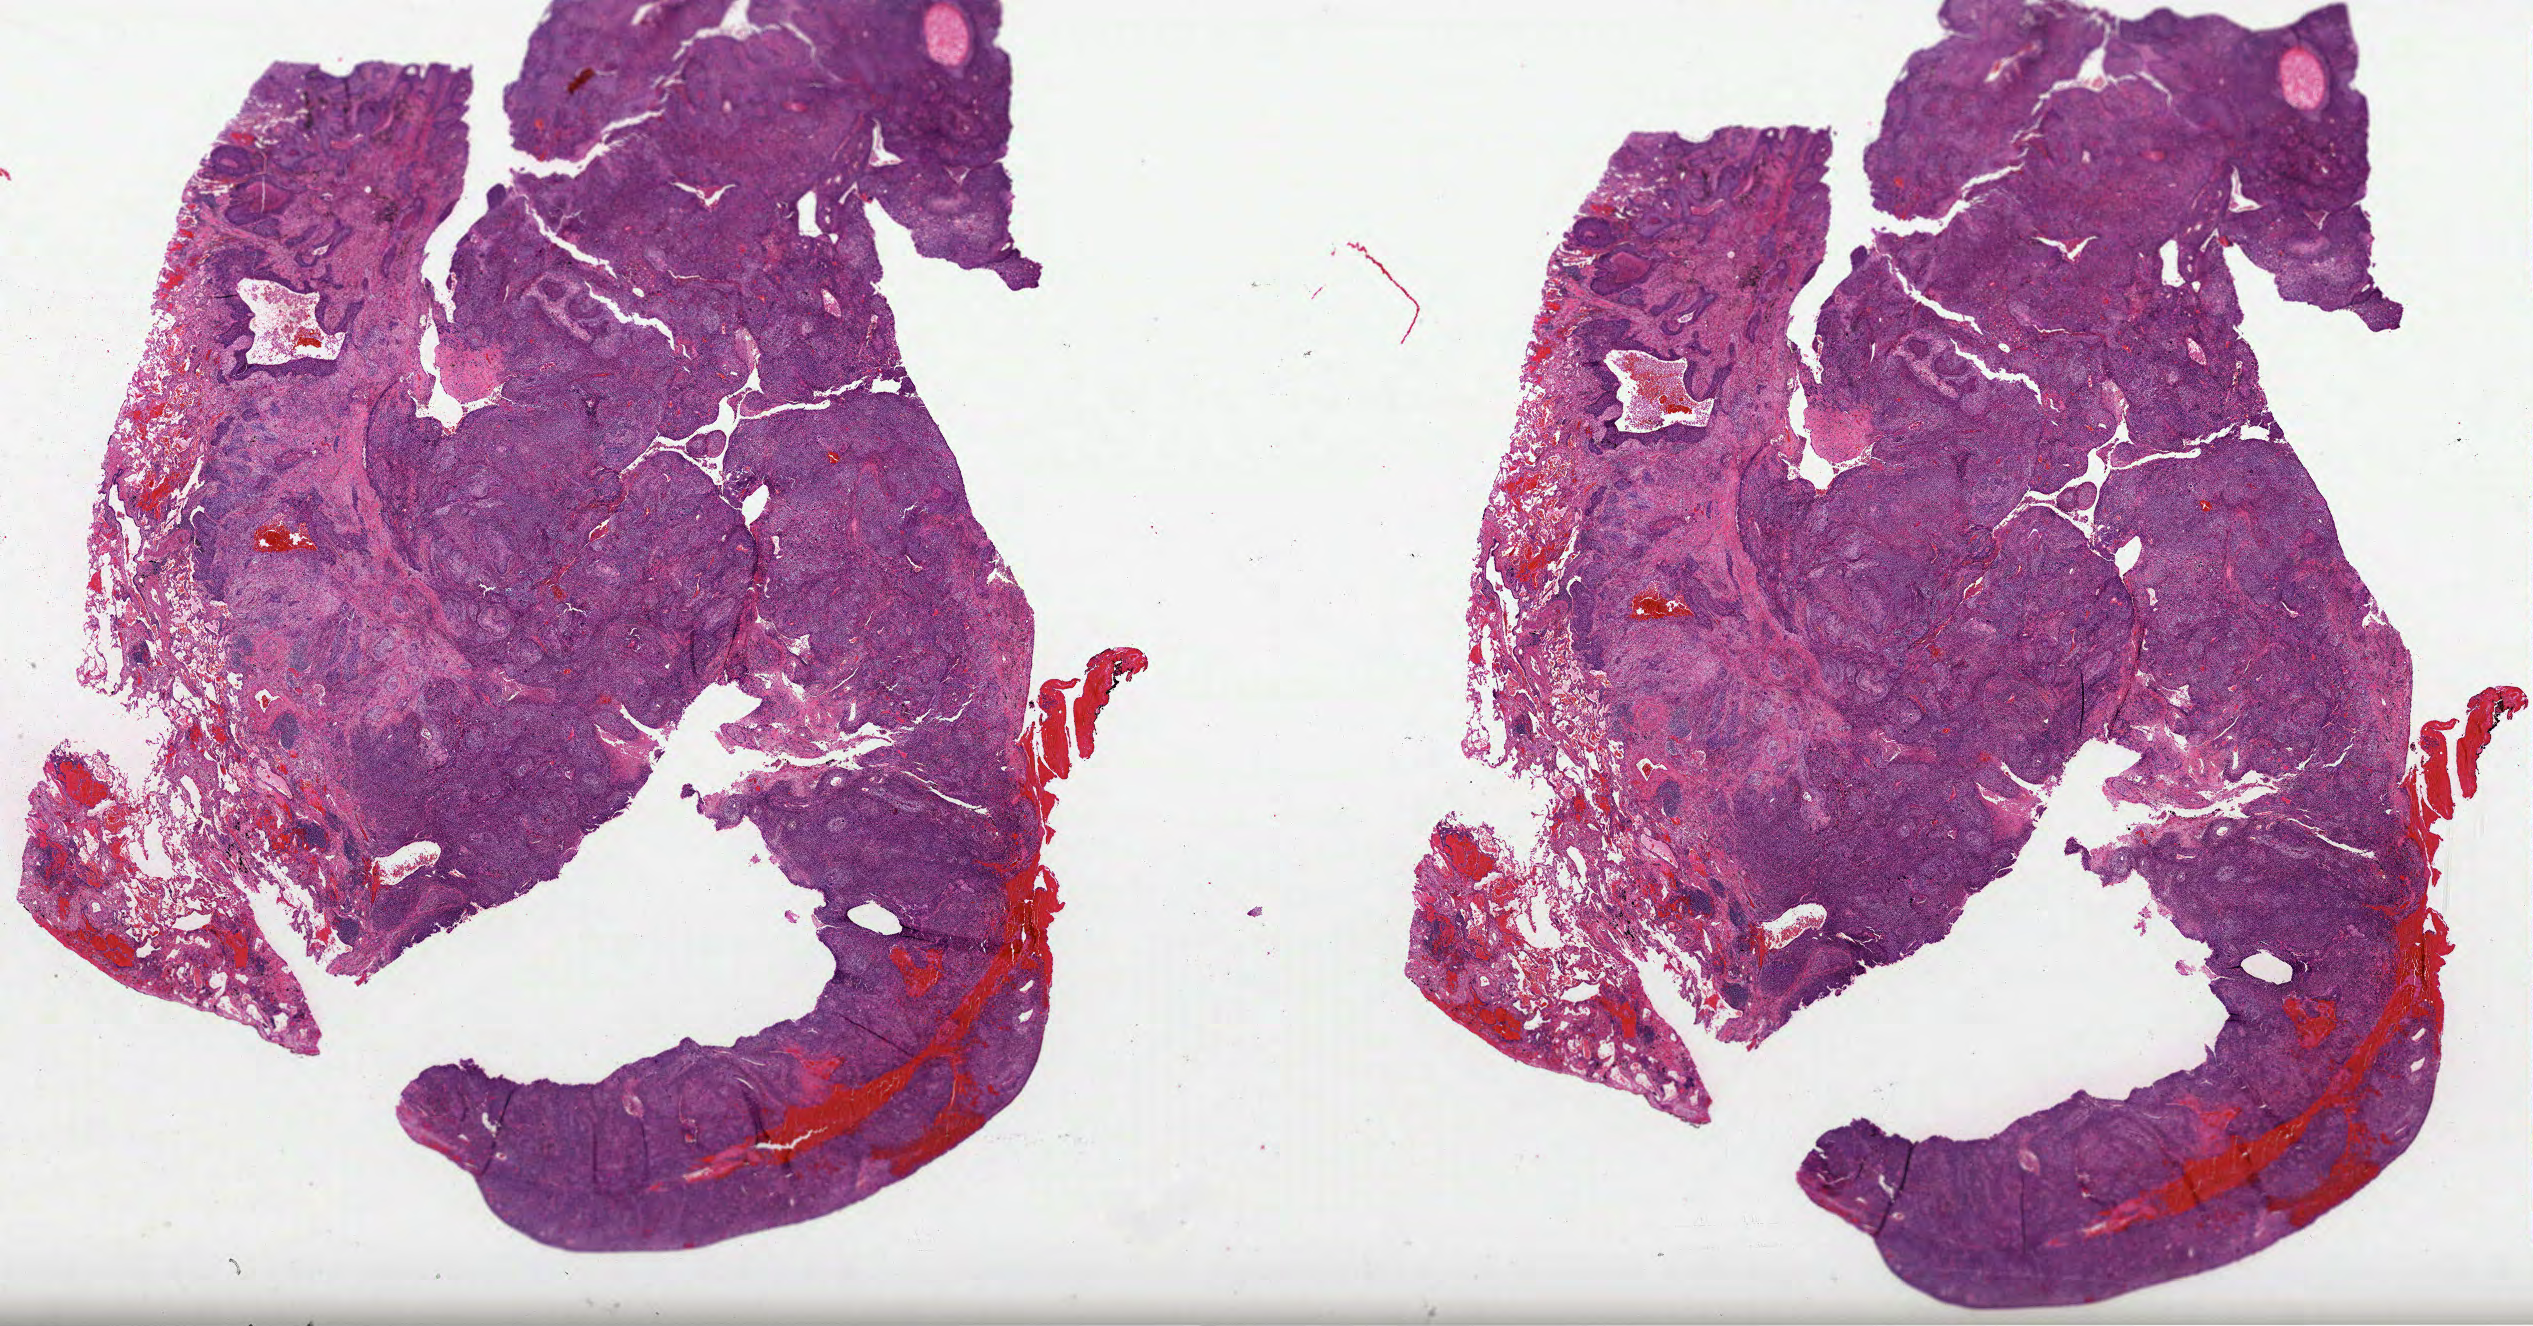
Digitized Hematoxylin and eosin (H&E) stained tissue section (whole slide) — whole scanned area (about 40.9 x 21.4 mm, from a 40x scan) shown as a low-resolution overview; formalin-fixed paraffin-embedded (FFPE) diagnostic section; lung, primary tumour sample. Female, age 76 years at initial diagnosis.
AJCC pathologic stage: IB (5th edition). Histologic diagnosis: Squamous cell carcinoma, NOS. Laterality: left.